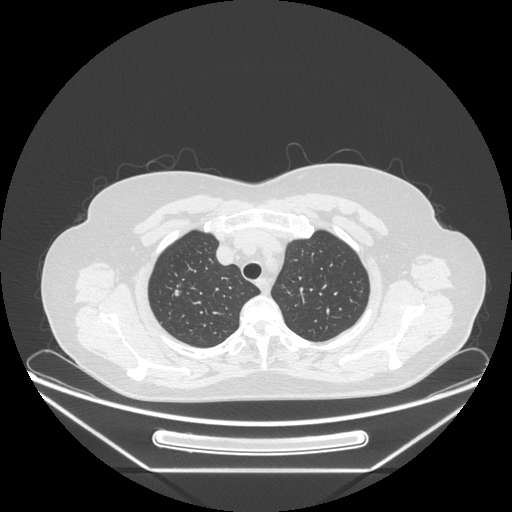
Chest CT, one axial slice. Position 202 of 236 along the scan axis. Reconstruction kernel STANDARD. 120 kVp. Lung window (W 1500 / L -600 HU). 1.25 mm slice thickness. 512 × 512 image matrix, field of view 433 × 433 mm. Female patient, age 60 years. Case-level facts recorded for this patient, not image findings: clinical TNM (as recorded): T1c N0 M0; histopathological grade: G2-3.
Annotated regions visible in this slice (rectangle marked by the reading radiologist):
- lung tumour (recorded histology: adenocarcinoma): bounding box (x1, y1, x2, y2) in pixels: (171, 284, 184, 303)